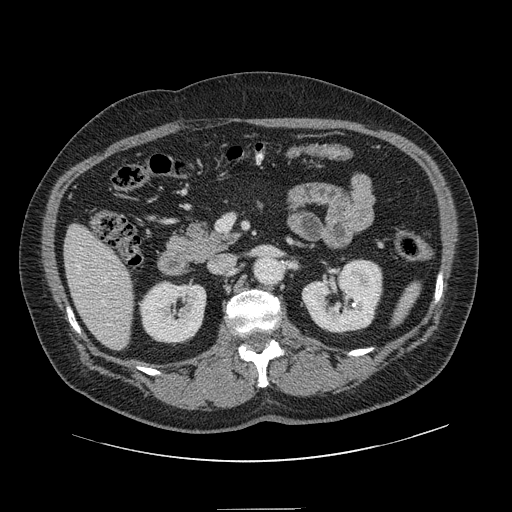
Contrast-enhanced abdominal CT, one axial slice; slice 56 of 154 in the series (ordered by position); intravenous contrast given; soft-tissue window (W 400 / L 40 HU); 2.5 mm slice thickness; 512 × 512 image matrix. Male patient, age 61 years. Case-level facts recorded for this patient, not image findings: diagnosis: colorectal cancer liver metastases, imaged before liver resection; multiple liver metastases: yes; largest metastasis: 2.6 cm; chemotherapy before resection: no.
Annotated regions visible in this slice (expert manual segmentation):
- hepatic veins: box from (x=77, y=265) to (x=105, y=304) px
- liver: (x=65, y=226)–(x=134, y=350)
- planned liver remnant (the part of the liver to remain after resection): (x=65, y=226)–(x=134, y=350)